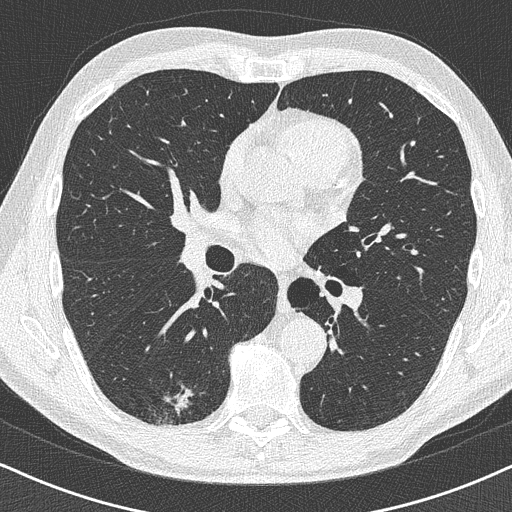
Low-dose screening chest CT, axial slice. Baseline annual screen. Lung window (W 1500 / L -600 HU). 1 mm slice thickness. 120 kVp. Slice 205 of 438 in the series. Male, age 63 years at enrolment.
Expert-annotated lung lesion, bounding box <140,375,211,430> (left, top, right, bottom; pixels). The exam's reader record, not a measurement of the box and not confirmed to be the same lesion: non-calcified nodule or mass ≥4 mm, right lower lobe, 16 × 13 mm, poorly defined margins. Official screen result: positive, change unspecified: nodule(s) >= 4 mm or enlarging nodule(s), mass(es), or other non-specific abnormalities suspicious for lung cancer. Later outcome: lung cancer diagnosed 74 days after this screen — adenocarcinoma, NOS, right lower lobe, moderately differentiated (G2), stage IA (AJCC 6th edition), 20 mm at pathology.